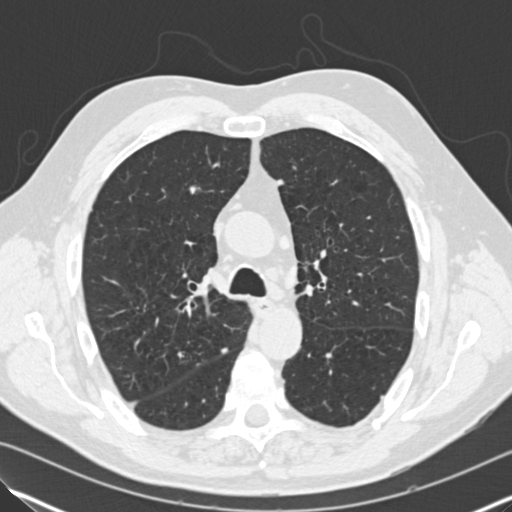
Axial slice from a low-dose chest CT screening exam; baseline screening round; lung window (W 1500 / L -600 HU); 2 mm slice thickness; standard (soft-tissue) reconstruction kernel (B30f); 140 kVp; 512 × 512 image matrix, field of view 340 × 340 mm. Male, age 65 years at enrolment. Former smoker at enrolment.
Lesion marked by an expert reader, bounding box (x1, y1, x2, y2) in pixels: (162, 342, 203, 378). The screening reader recorded 5 non-calcified nodules or masses ≥4 mm on this exam; which of them this box marks is not recorded. Official screen result: positive, change unspecified: nodule(s) >= 4 mm or enlarging nodule(s), mass(es), or other non-specific abnormalities suspicious for lung cancer. Later outcome: lung cancer diagnosed 814 days after this screen (after the third annual screen) — adenocarcinoma, NOS, right upper lobe, moderately differentiated (G2), stage IA (AJCC 6th edition), 16 mm at pathology.